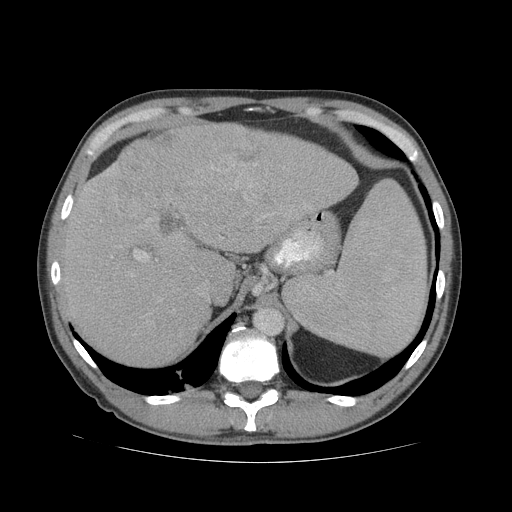
Contrast-enhanced abdominal CT (liver protocol), one axial slice; position 51 of 81 along the scan axis; reconstruction kernel STANDARD; 140 kVp; soft-tissue window (W 400 / L 40 HU); 2.5 mm slice thickness; 512 × 512 image matrix, field of view 400 × 400 mm. From the clinical record (not read from this slice): diagnosis: hepatocellular carcinoma (patient treated with transarterial chemoembolisation; whether this scan precedes or follows treatment is not stated here); TNM stage (as recorded): Stage-IVB; Child-Pugh class: B; tumour differentiation: well differentiated; tumour nodularity: multinodular.
Annotated regions visible in this slice (semi-automatically segmented with operator editing):
- liver parenchyma outside the tumour (the mass and vessels are separate outlines, so this box may not span the whole liver): bounding box [x1, y1, x2, y2] px = [60, 124, 358, 366]
- mass: [108, 126, 261, 226]
- liver vessels: [85, 163, 310, 276]